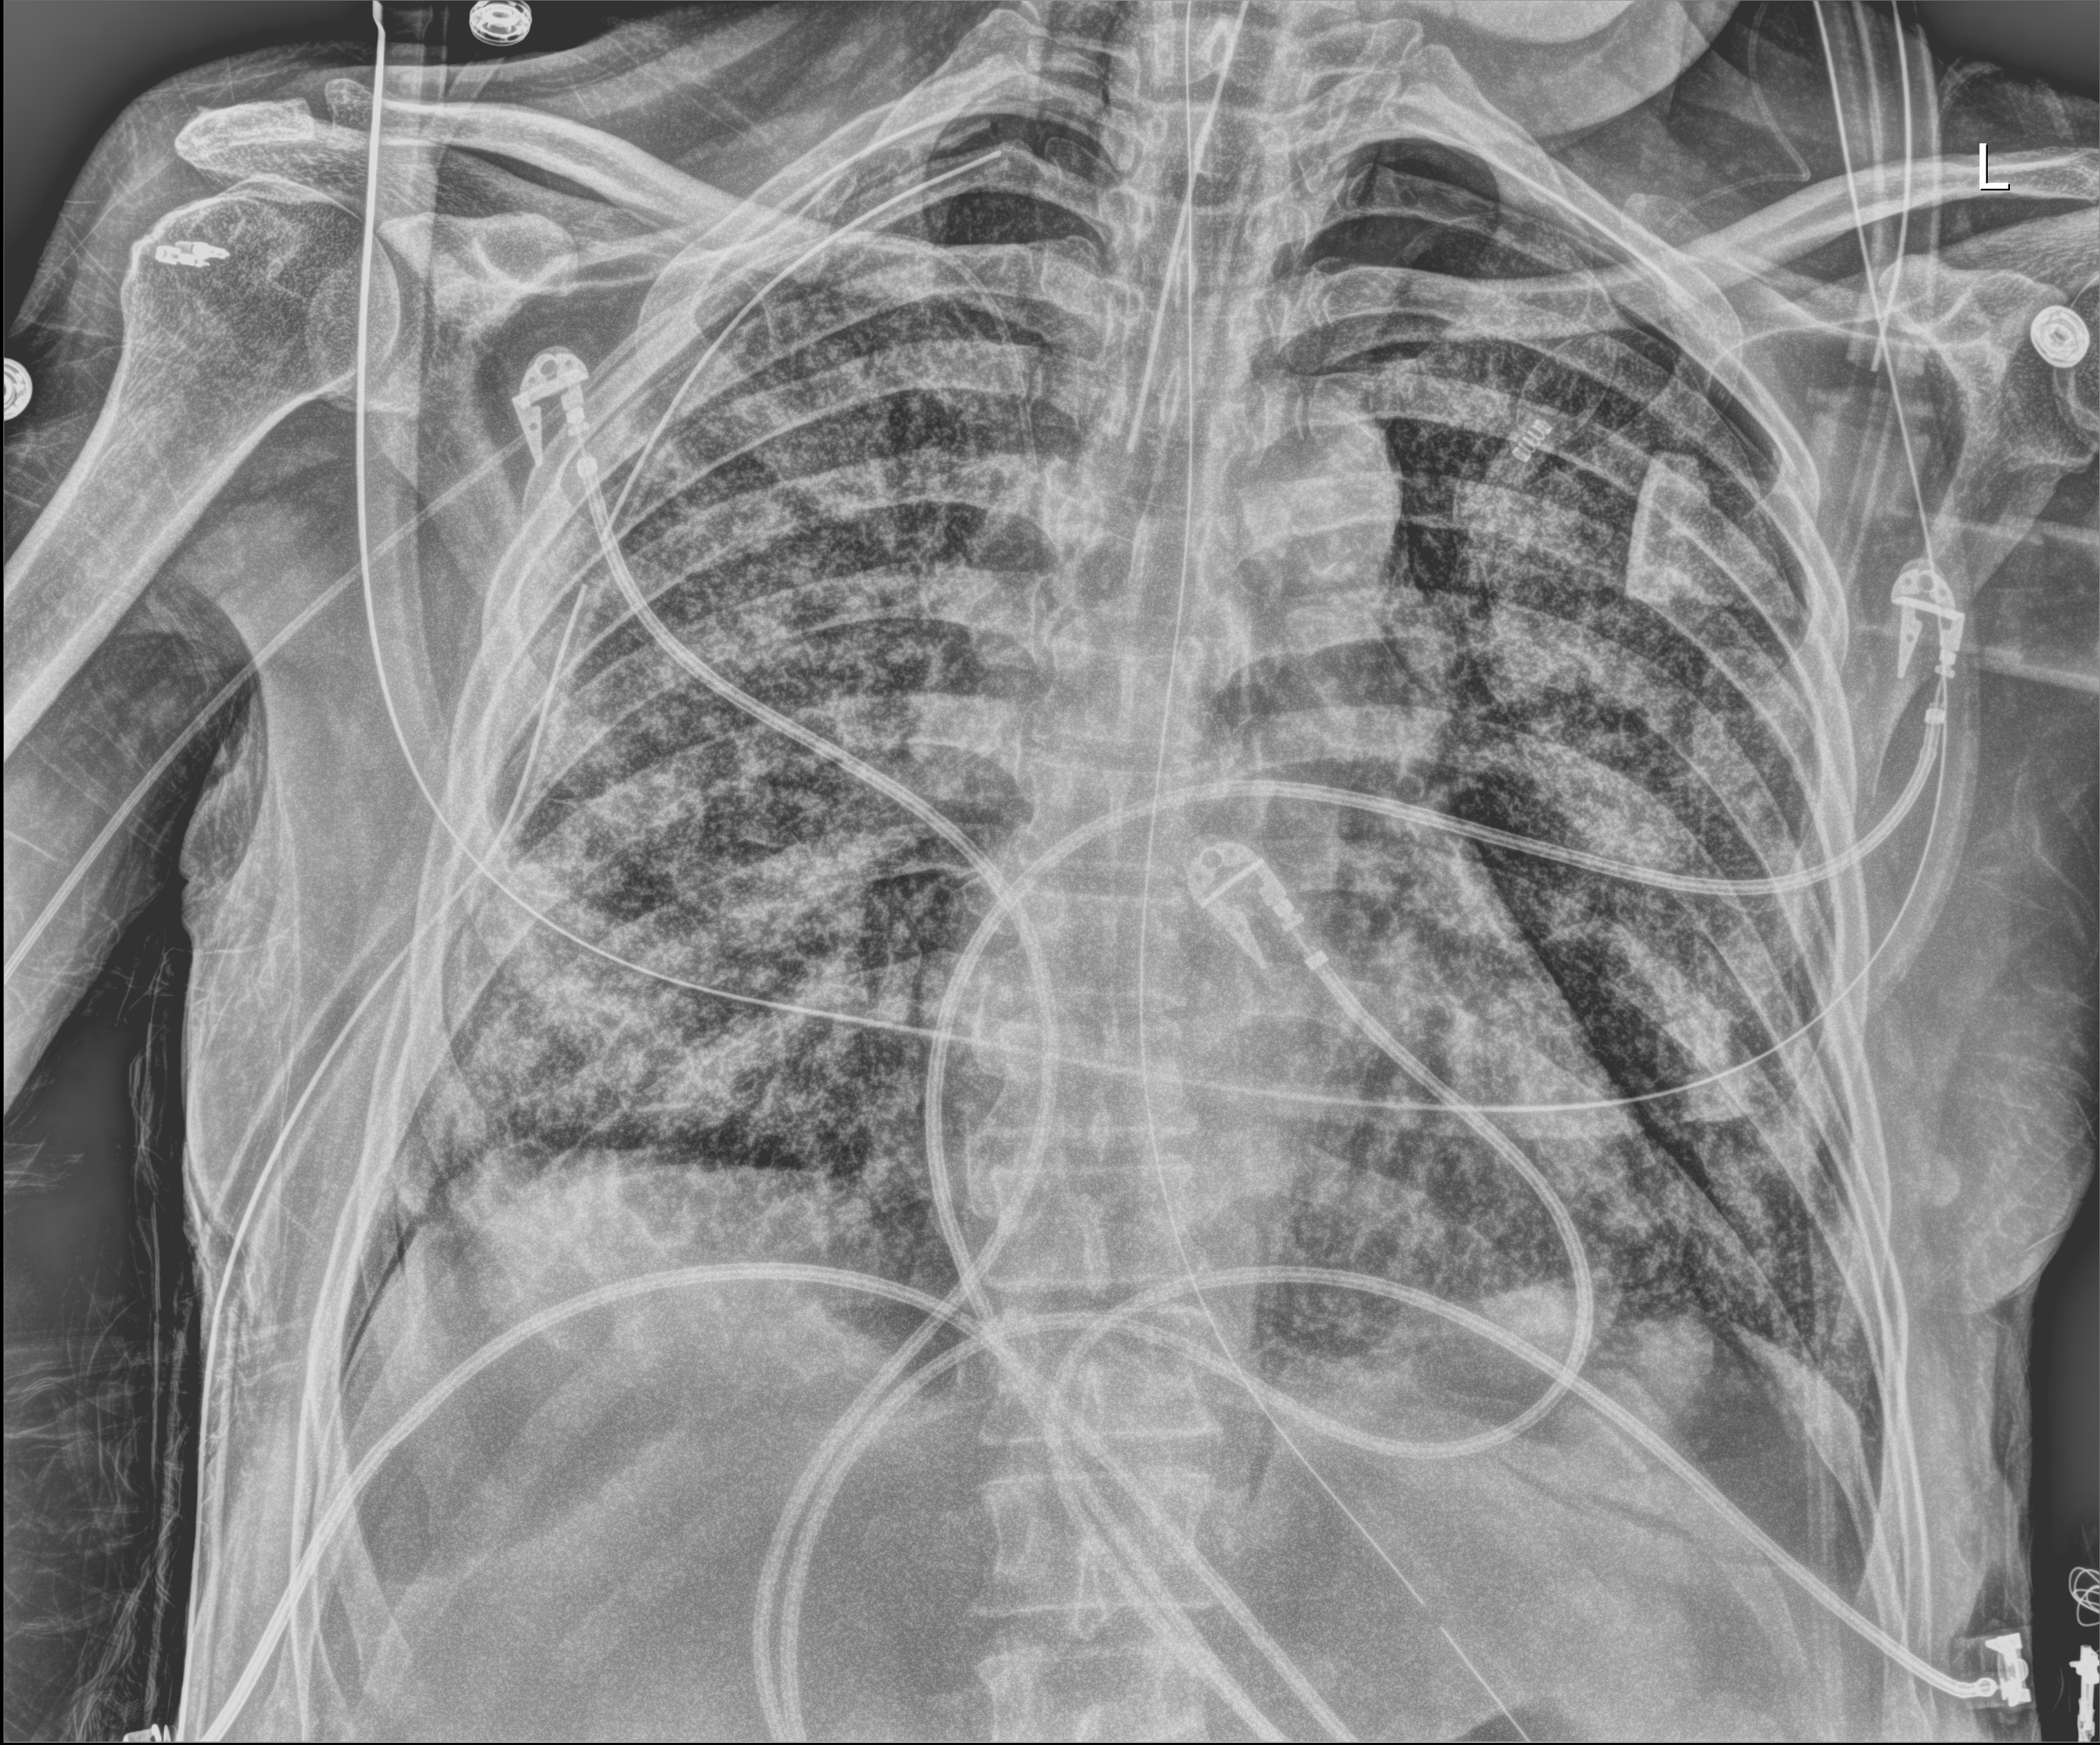
Bedside chest radiograph (digital radiography), anteroposterior (AP) projection. Male patient hospitalised with COVID-19, age 60–74 years.
Hospital-stay facts (about this admission, not read from this image; timing relative to this image not recorded): length of hospital stay: 65 days; admitted to intensive care during this hospital stay: yes; mechanically ventilated during this hospital stay: yes.